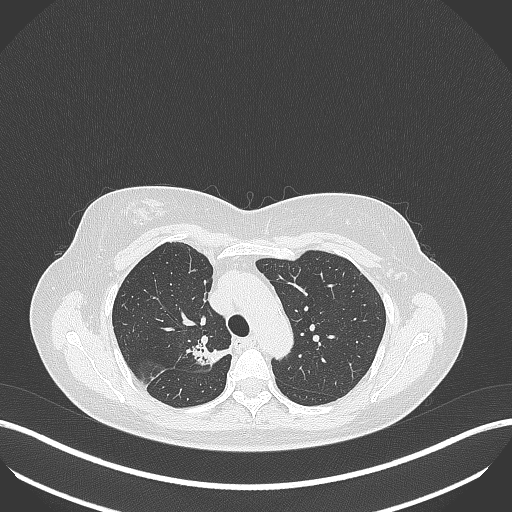
Chest CT, one axial slice; position 287 of 386 along the scan axis; reconstruction kernel B70f; lung window (W 1500 / L -600 HU); 1 mm slice thickness; 512 × 512 image matrix, field of view 400 × 400 mm. Female patient, age 65 years. From the clinical record (not read from this slice): clinical TNM (as recorded): T1b N0 M0; histopathological grade: G2.
Structures marked on this image (rectangle marked by the reading radiologist):
- lung tumour (recorded histology: adenocarcinoma): bounding box [x1, y1, x2, y2] px = [190, 338, 233, 370]